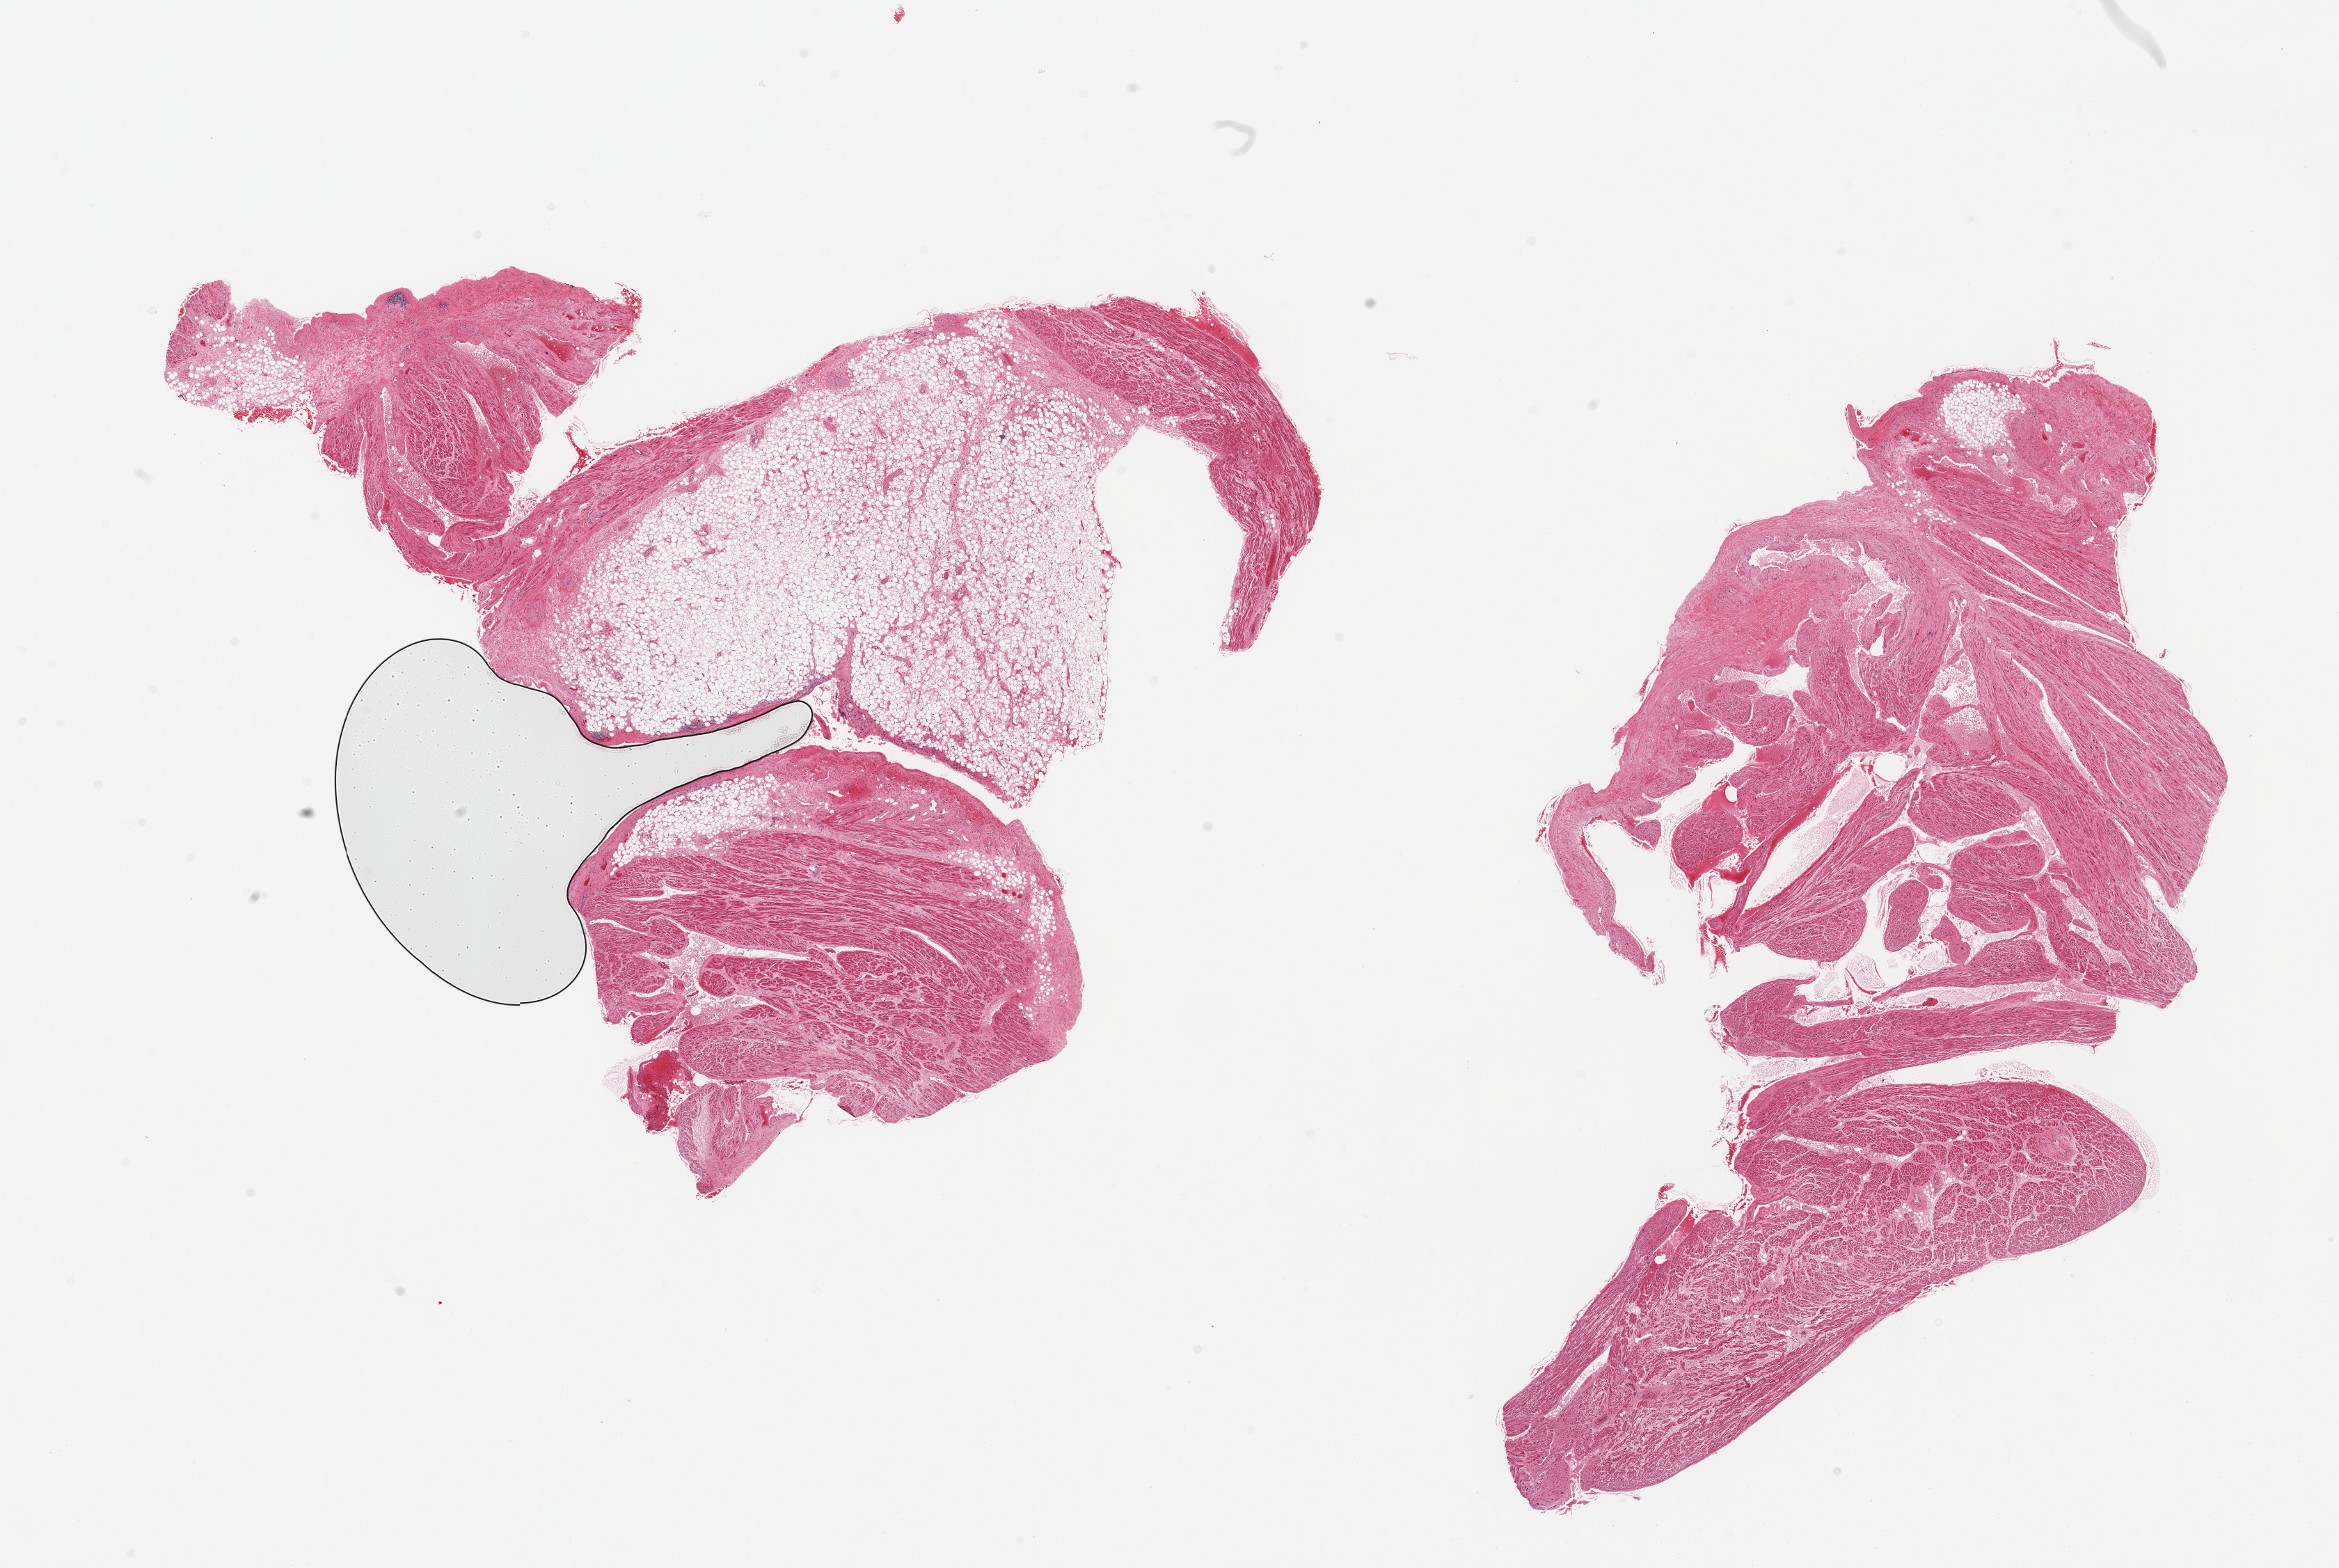
Digitized haematoxylin and eosin-stained section, brightfield — shown as a low-resolution overview of the whole scanned area (about 26.6 x 17.8 mm, slide scanned at 20x), PAXgene-fixed, paraffin-embedded tissue, sampled site (target tissue): auricular appendage, donor tissue sample. Donor: male.
Reviewer comment on this tissue sample: 2 pieces; 1 piece has 60% external fat, other has 10% external fibrofatty content.